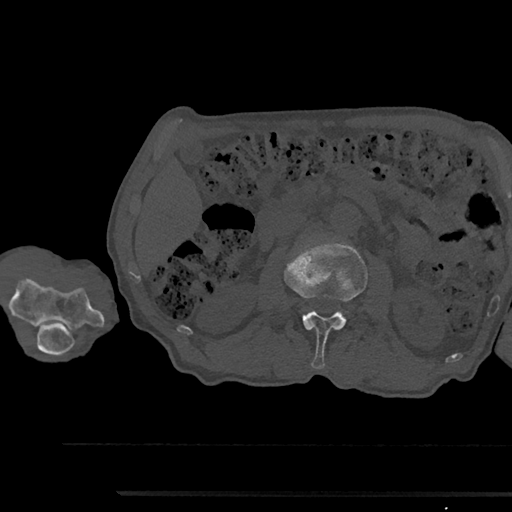
CT including the spine, one axial slice. Slice 551 of 797 in the series (ordered by position). 120 kVp. Bone window (W 1800 / L 400 HU). 0.5 mm slice thickness. 512 × 512 image matrix. Patient: male, 79 years. Case-level facts recorded for this patient, not image findings: primary cancer: prostate.
Annotated regions visible in this slice (semi-automatic segmentation, software-assisted and operator-edited):
- L2 vertebra: bounding box <285,243,367,369> (left, top, right, bottom; pixels)